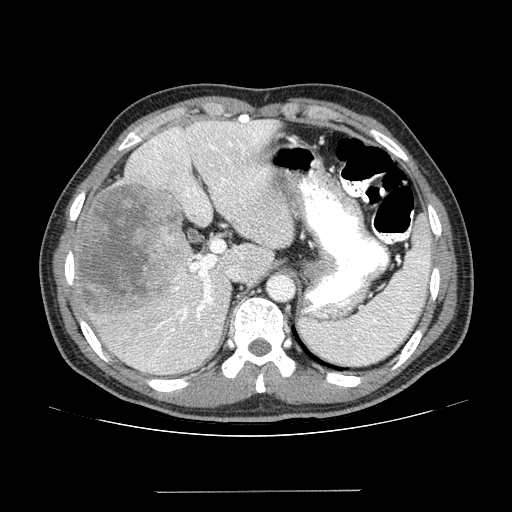
Contrast-enhanced abdominal CT (liver protocol), one axial slice; position 97 of 131 along the scan axis; one of 2 acquisitions stored at this slice position; soft-tissue window (W 400 / L 40 HU); 2.5 mm slice thickness; 512 × 512 image matrix. Case-level facts recorded for this patient, not image findings: diagnosis: hepatocellular carcinoma (patient treated with transarterial chemoembolisation; whether this scan precedes or follows treatment is not stated here); TNM stage (as recorded): Stage-I; Child-Pugh class: A.
Structures marked on this image (semi-automatically segmented with operator editing):
- liver parenchyma outside the tumour (the mass and vessels are separate outlines, so this box may not span the whole liver): box from (x=72, y=120) to (x=292, y=374) px
- mass: (x=76, y=183)–(x=190, y=319)
- liver vessels: (x=126, y=121)–(x=284, y=370)